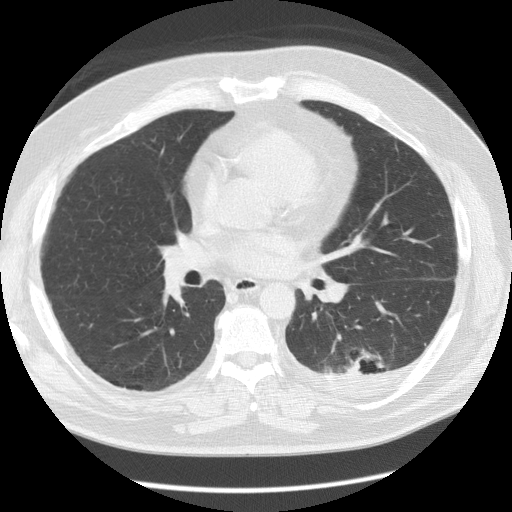
Low-dose screening chest CT, one axial slice; position 67 of 126 along the scan axis; reconstruction kernel STANDARD; lung window (W 1500 / L -600 HU); 512 × 512 image matrix, field of view 370 × 370 mm.
Annotated regions visible in this slice (manually delineated by an expert):
- lesion 1 (tumor, lower lobe of left lung): bounding box (x1, y1, x2, y2) in pixels: (343, 355, 366, 375)